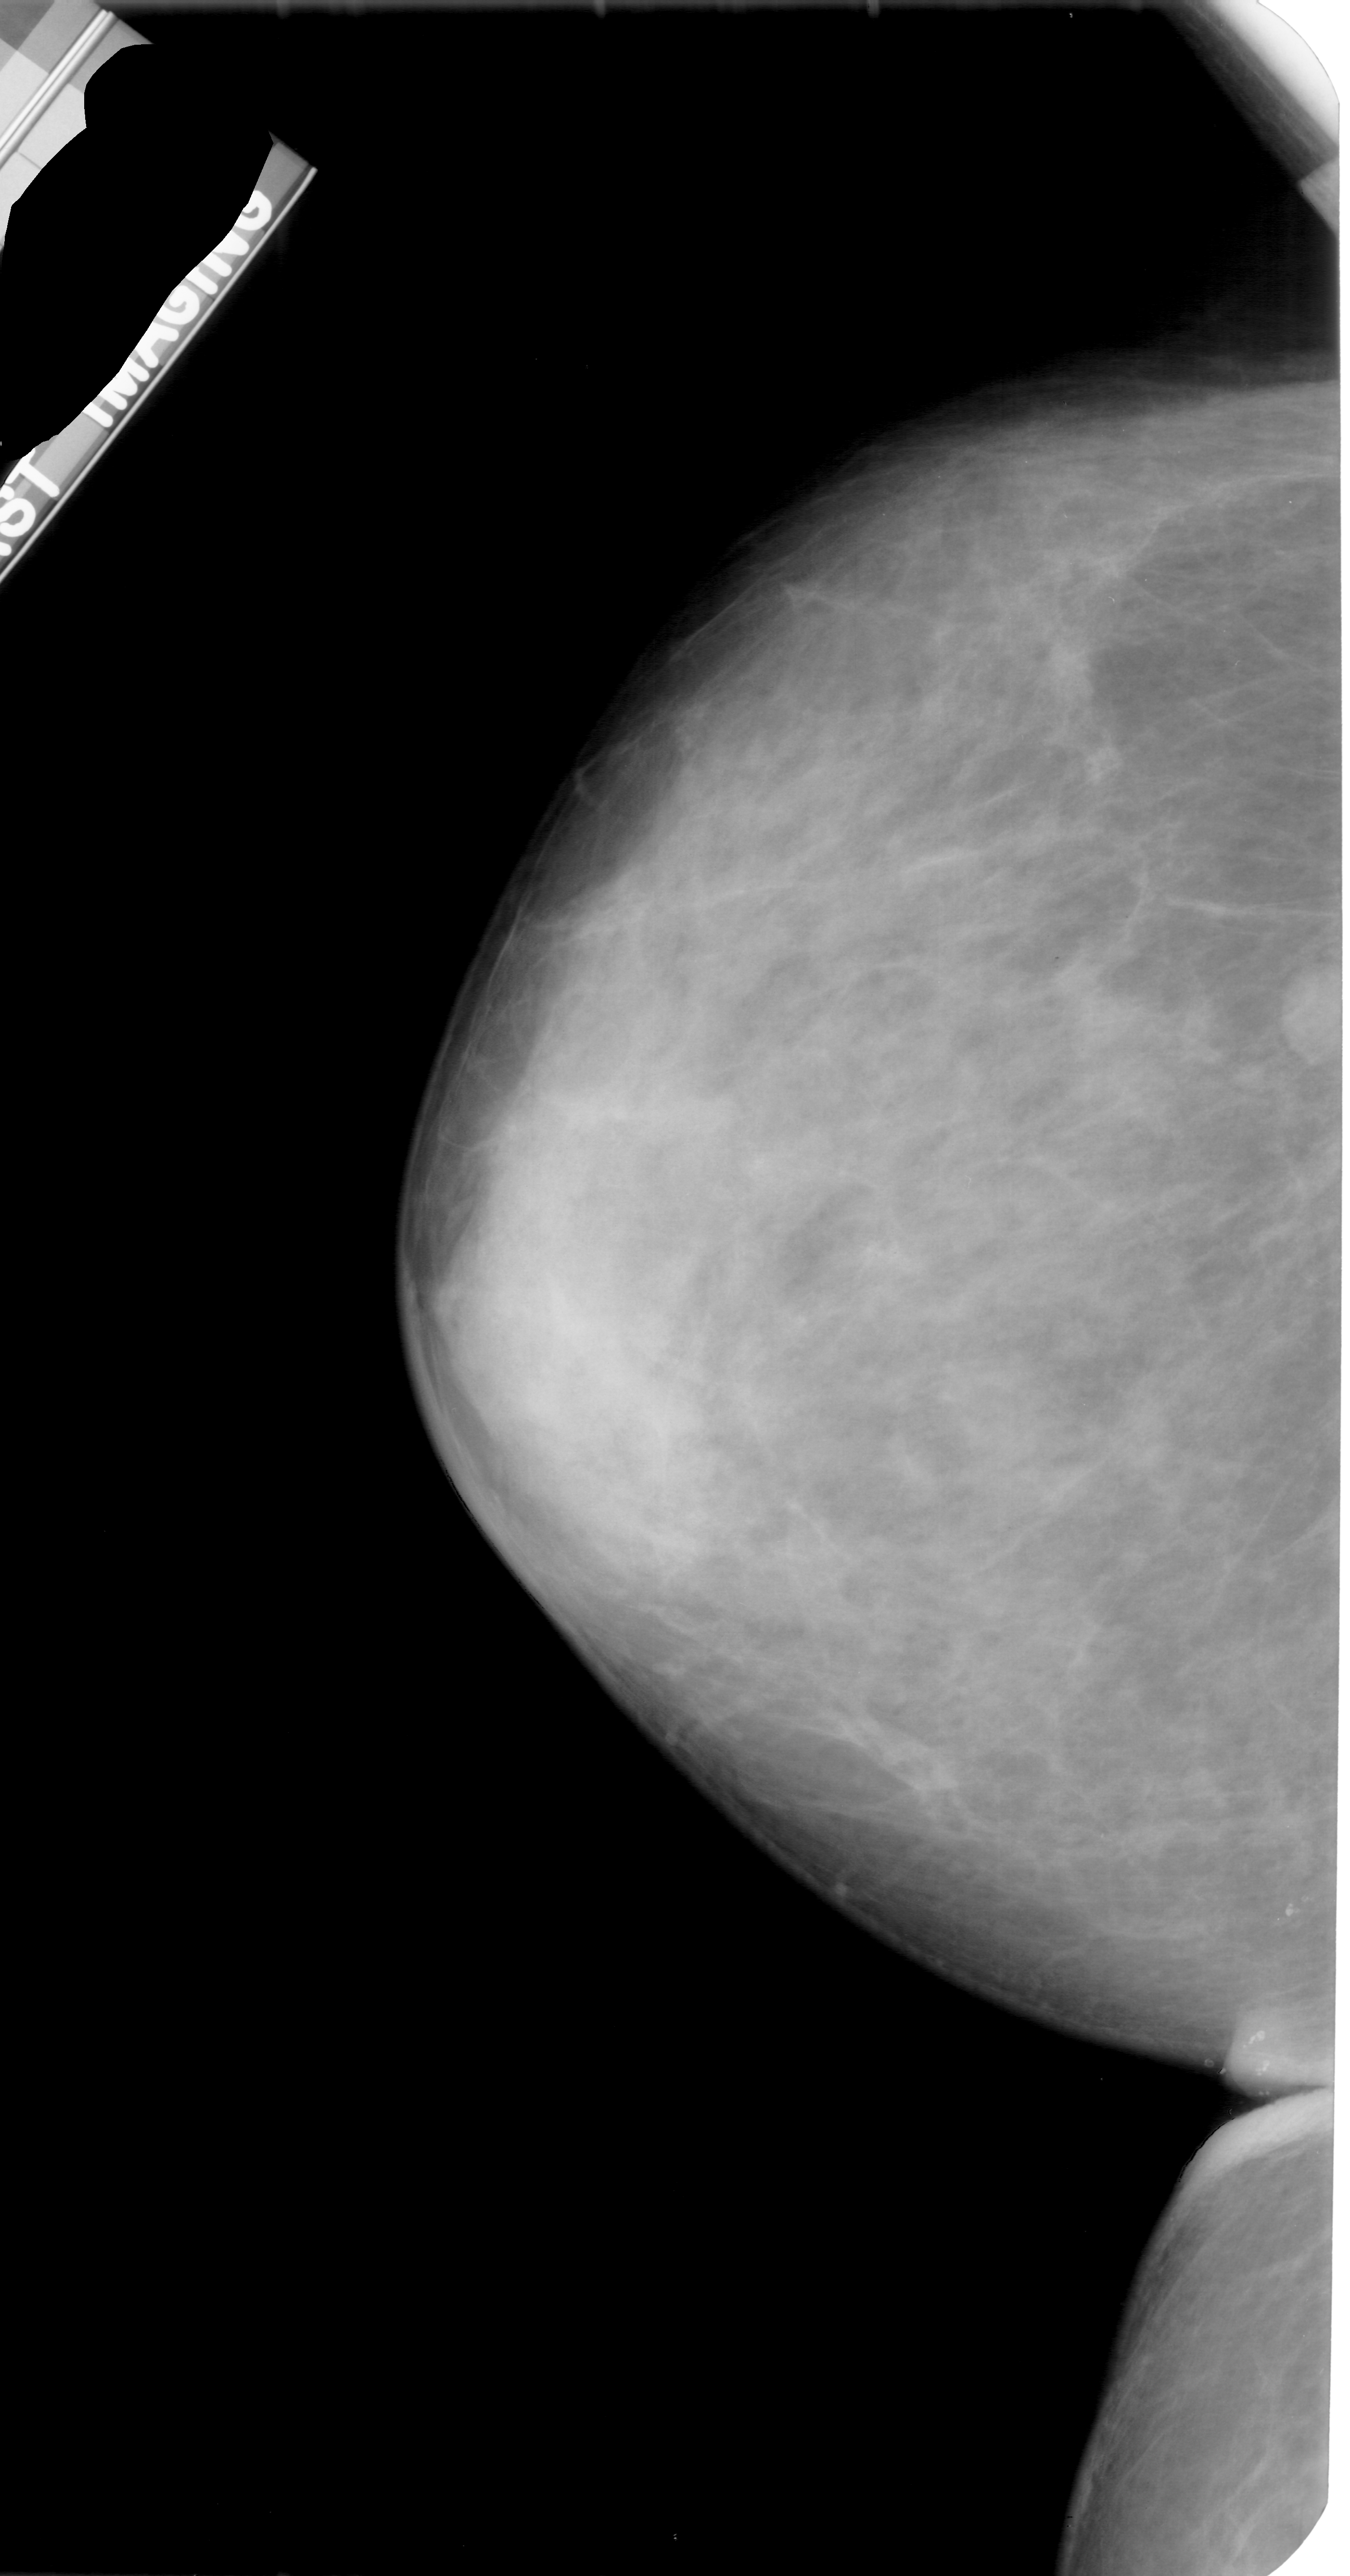
Scanned film-screen mammogram. Left breast. Craniocaudal (CC) view. BI-RADS breast density category 3 (scale 1–4). 1350 × 2576 image matrix.
Marked abnormalities (boxes around the expert regions of interest):
- mass, shape round, margins circumscribed; BI-RADS assessment category 3; pathology (as recorded): benign: bounding box (x1, y1, x2, y2) in pixels: (1261, 957, 1336, 1069)